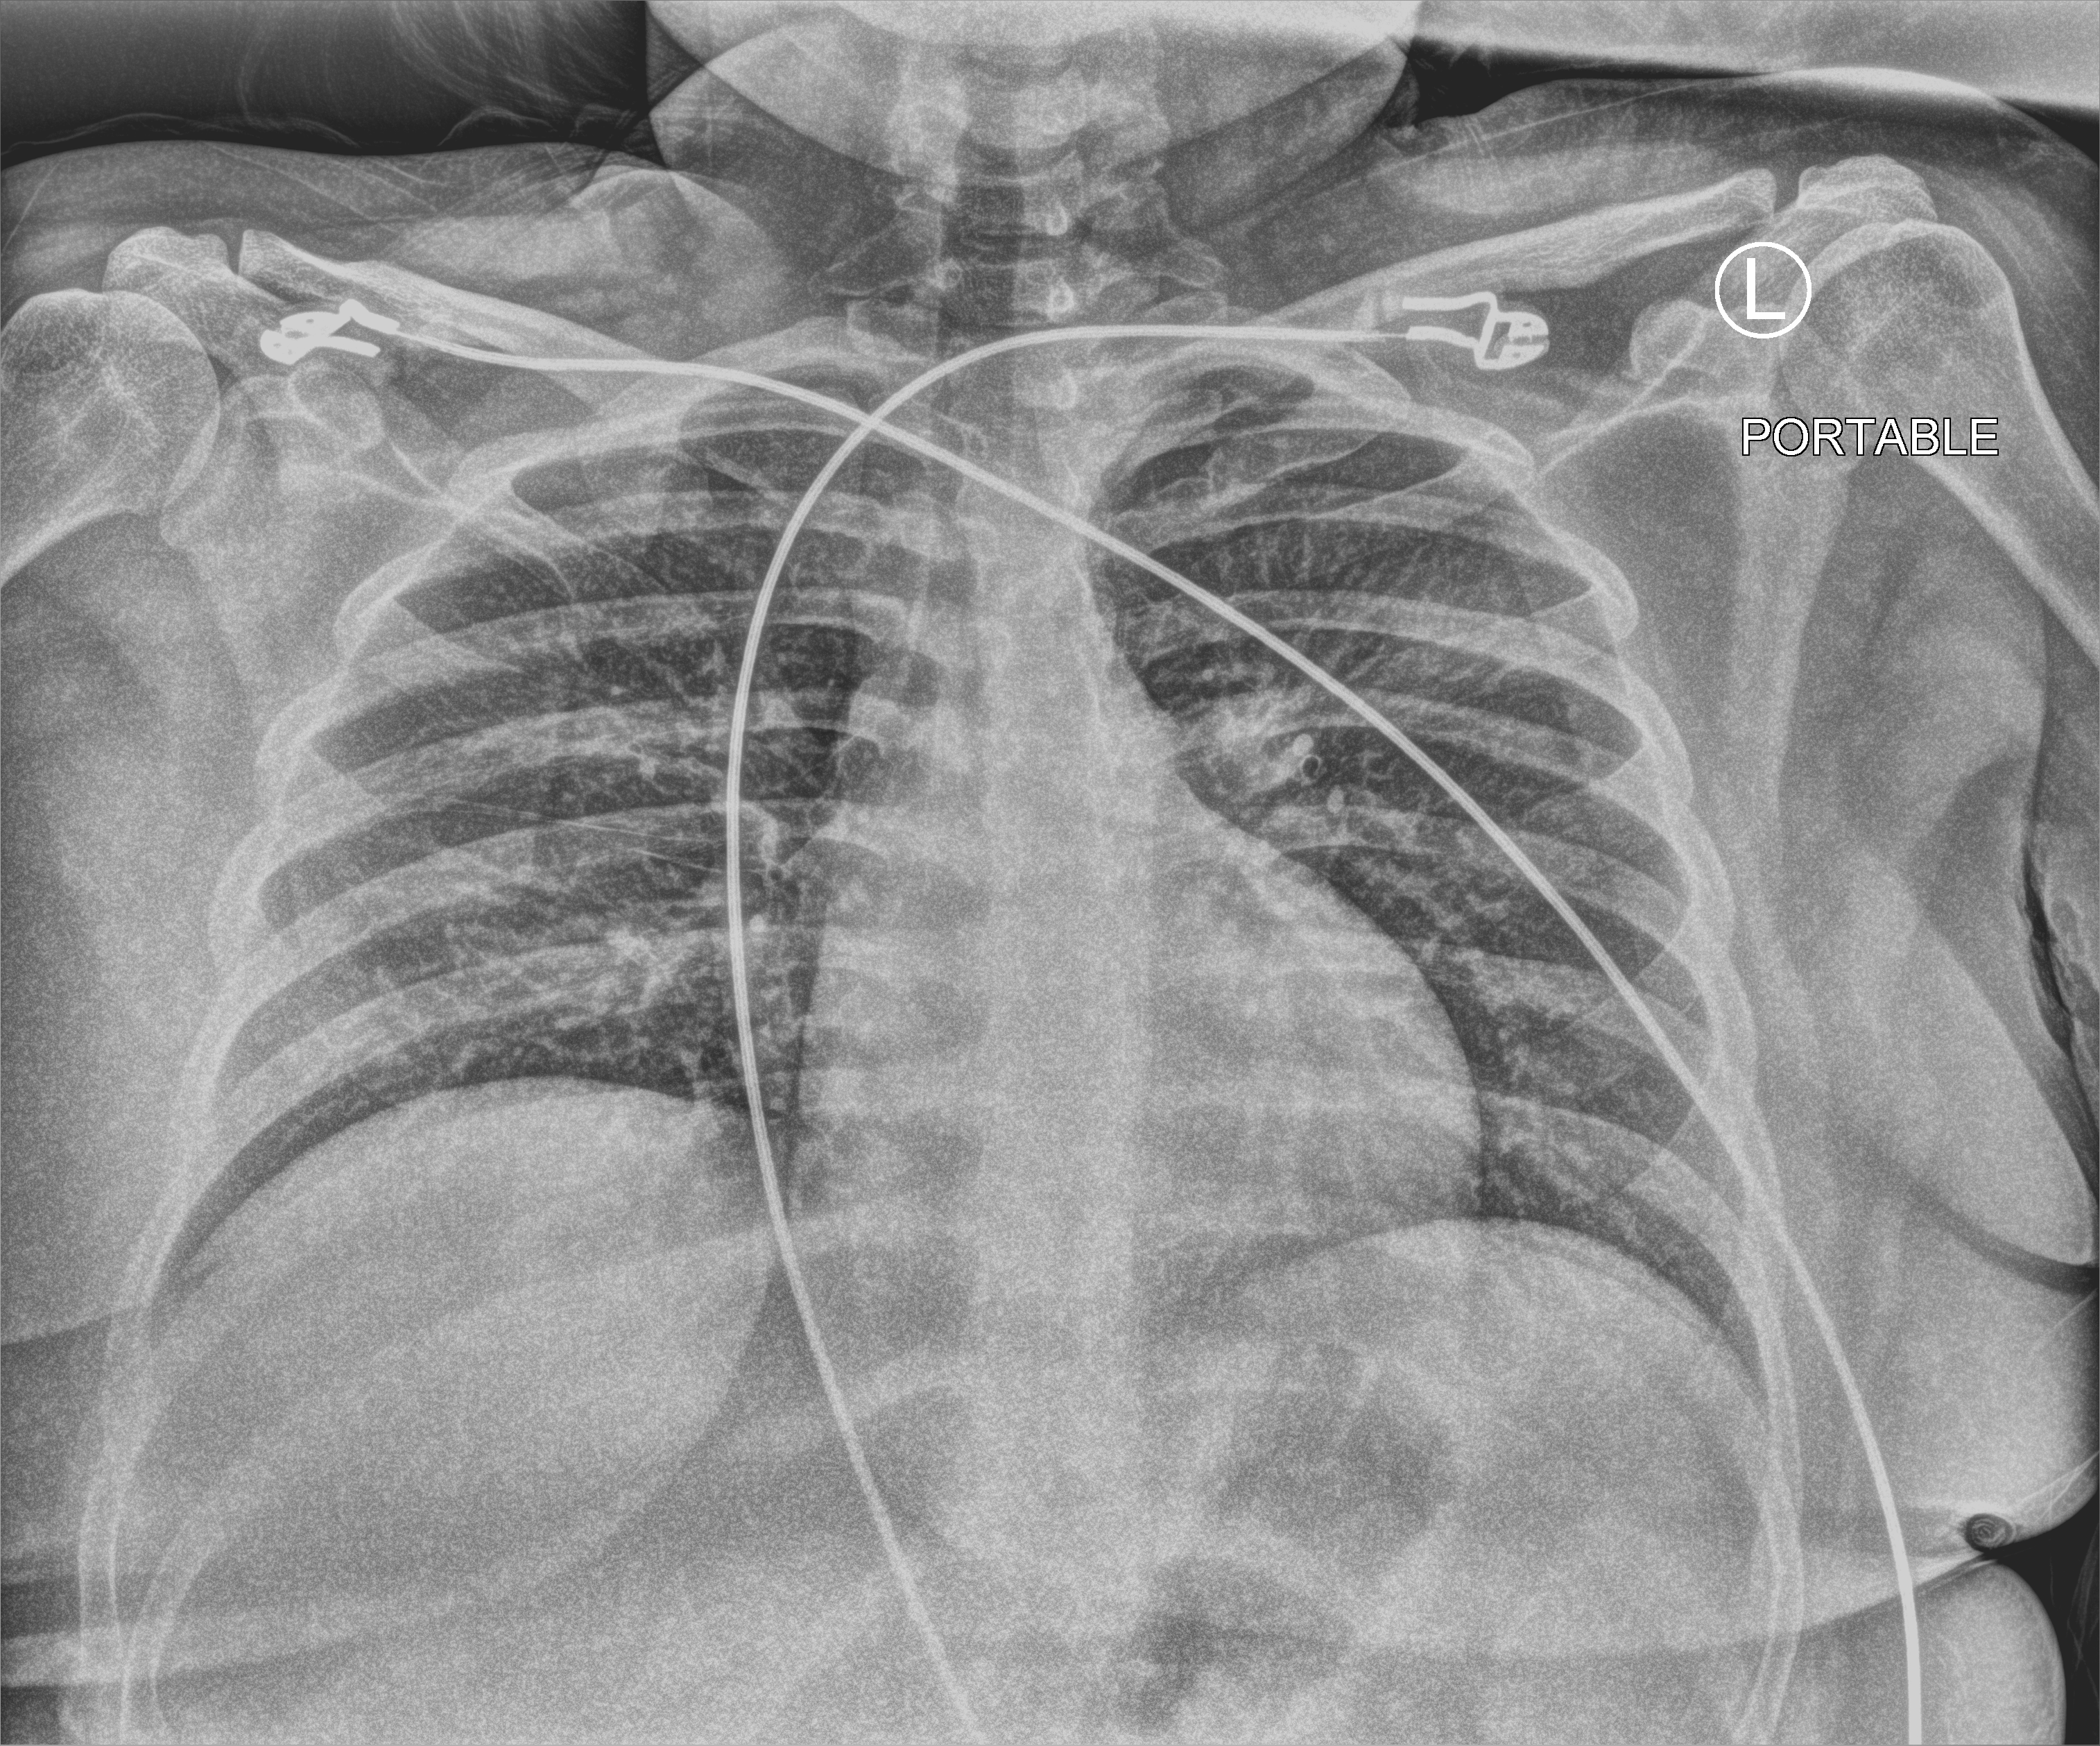
Portable chest radiograph, anteroposterior (AP) projection. Patient hospitalised with COVID-19; female, aged 18–59 years.
Hospital-stay facts (about this admission, not read from this image; timing relative to this image not recorded): admitted to intensive care during this hospital stay: no; mechanically ventilated during this hospital stay: no.